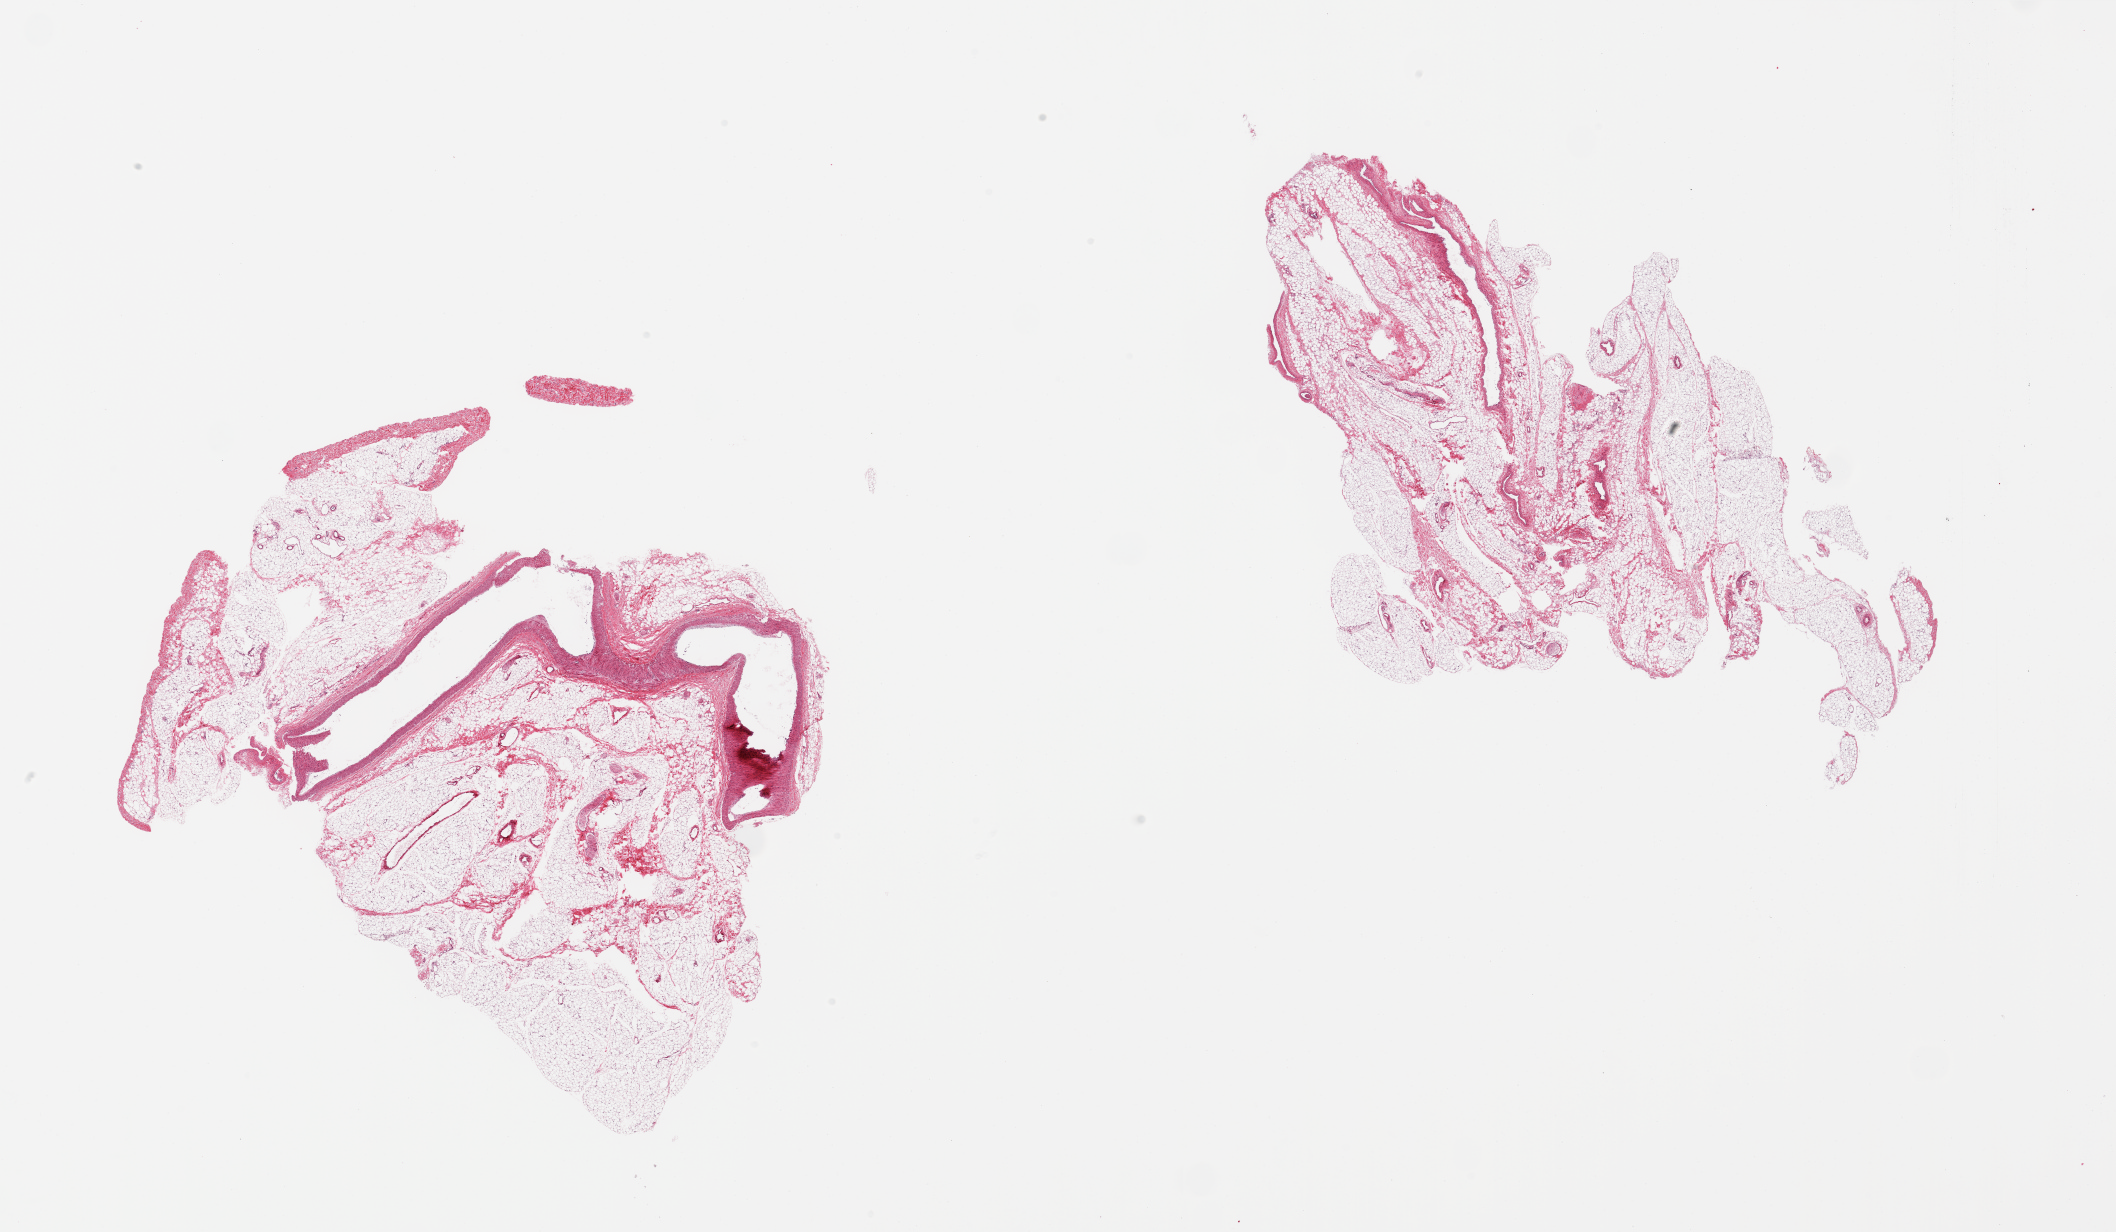
Digitized H&E-stained section, whole scanned area (about 33.5 x 19.5 mm, slide scanned at 20x) shown as a low-resolution overview, PAXgene-fixed, paraffin-embedded tissue, target tissue: omentum, donor tissue sample. Donor sex: female.
Reviewer comment on this tissue sample: 2 pieces, ~10% vascular/fibrous tissue.